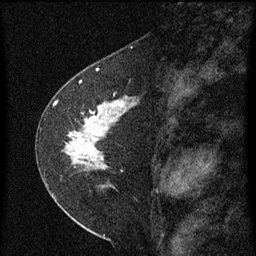
Breast MRI (dynamic contrast-enhanced), one sagittal slice; slice 33 of 60 in the series (ordered by position); dynamic contrast-enhanced series, image 2 of 3 at this slice position (ordered by acquisition); 1.5 T; TE 4.2 ms, TR 8 ms; 2 mm slice thickness; 256 × 256 image matrix, field of view 180 × 180 mm. Female patient, age 47 years.
Outlined on this slice (semi-automatic segmentation, software-assisted and operator-edited):
- analysis volume of interest (the breast-tissue region the enhancement analysis was run in; not a lesion): bounding box (x1, y1, x2, y2) in pixels: (44, 84, 141, 199)
- tumour enhancement mask (voxels above the 70 % enhancement threshold inside the analysis volume of interest): (68, 96, 127, 169)